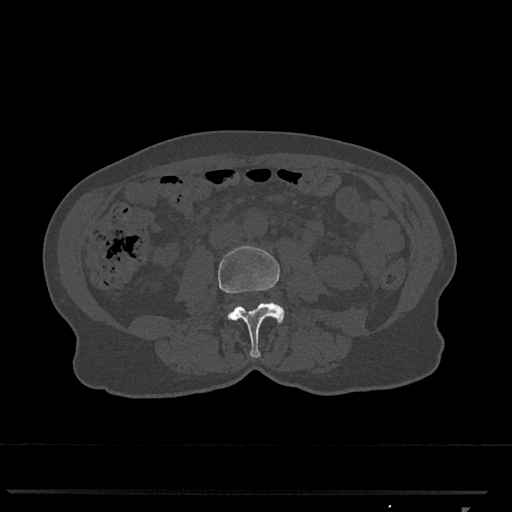
CT including the spine, one axial slice. Position 262 of 793 along the scan axis. Bone window (W 1800 / L 400 HU). 512 × 512 image matrix. Patient: female, 62 years. From the clinical record (not read from this slice): primary cancer: renal.
Outlined on this slice (semi-automatically segmented with operator editing):
- L3 vertebra: bounding box <218,246,285,358> (left, top, right, bottom; pixels)